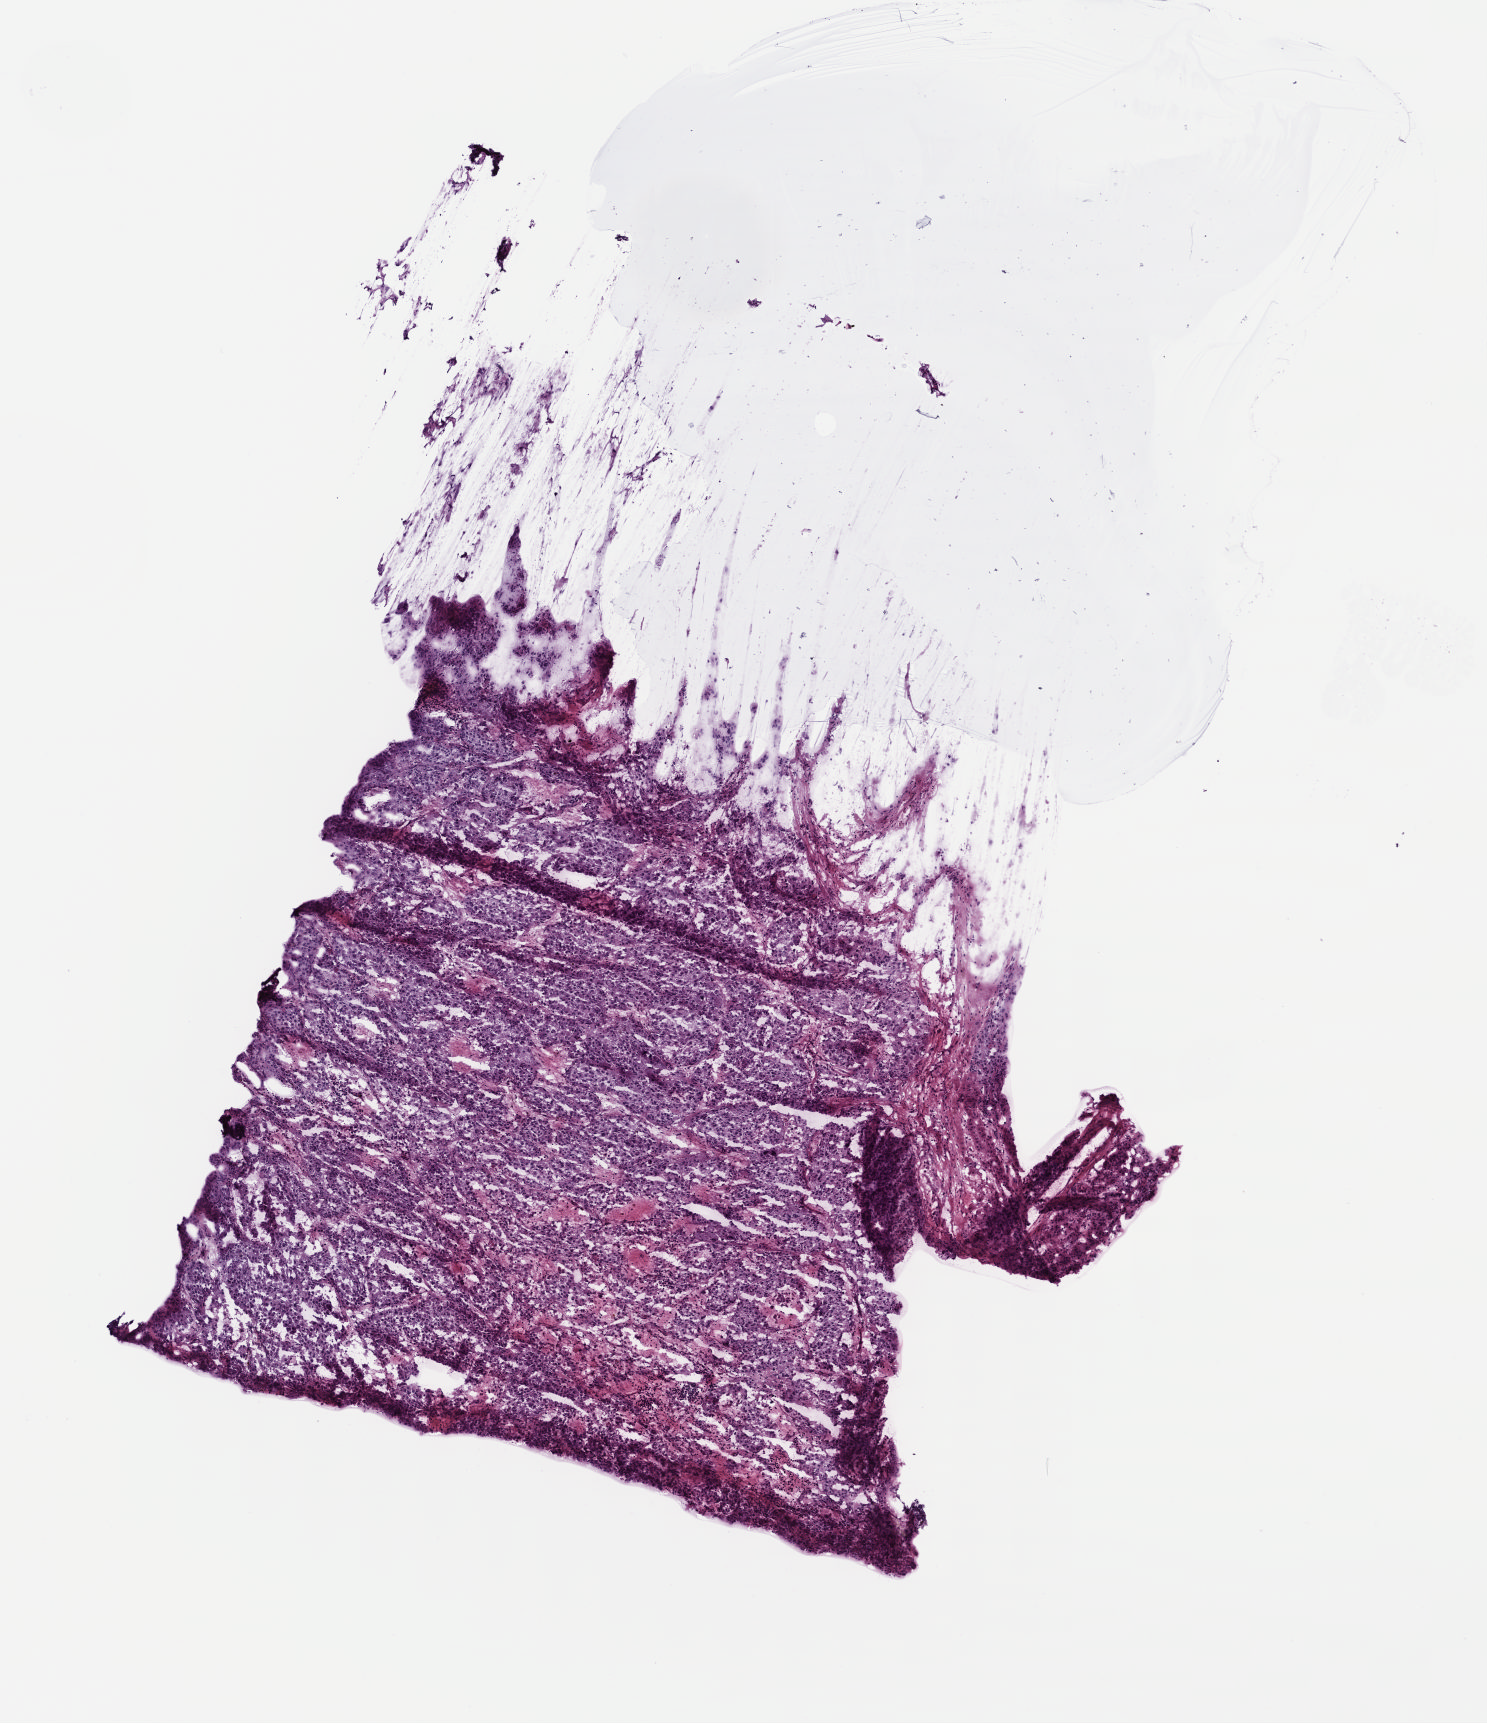
Digitized H&E tissue section (whole slide), whole scanned area (about 5.8 x 6.8 mm, from a 40x scan) shown as a low-resolution overview; frozen section; adrenal gland, primary tumour sample. Female, age 46 years at initial diagnosis. Slide review estimates, as recorded: tumour cells 80%, tumour nuclei 88%.
Pathologic diagnosis: Pheochromocytoma, NOS.